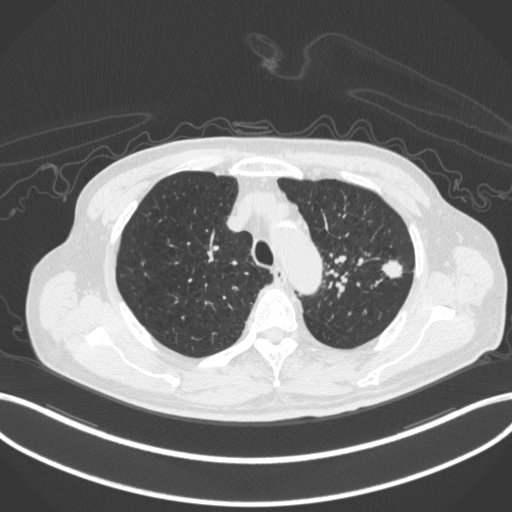
Chest CT, one axial slice. Slice 344 of 420 in the series (ordered by position). Reconstruction kernel B31f. 120 kVp. Lung window (W 1500 / L -600 HU). 1 mm slice thickness. 512 × 512 image matrix, field of view 400 × 400 mm. Patient: male, 77 years. From the clinical record (not read from this slice): clinical TNM (as recorded): T3 N1 M0.
Annotated regions visible in this slice (bounding box drawn by a radiologist):
- lung tumour (recorded histology: adenocarcinoma): bounding box (x1, y1, x2, y2) in pixels: (380, 259, 406, 282)